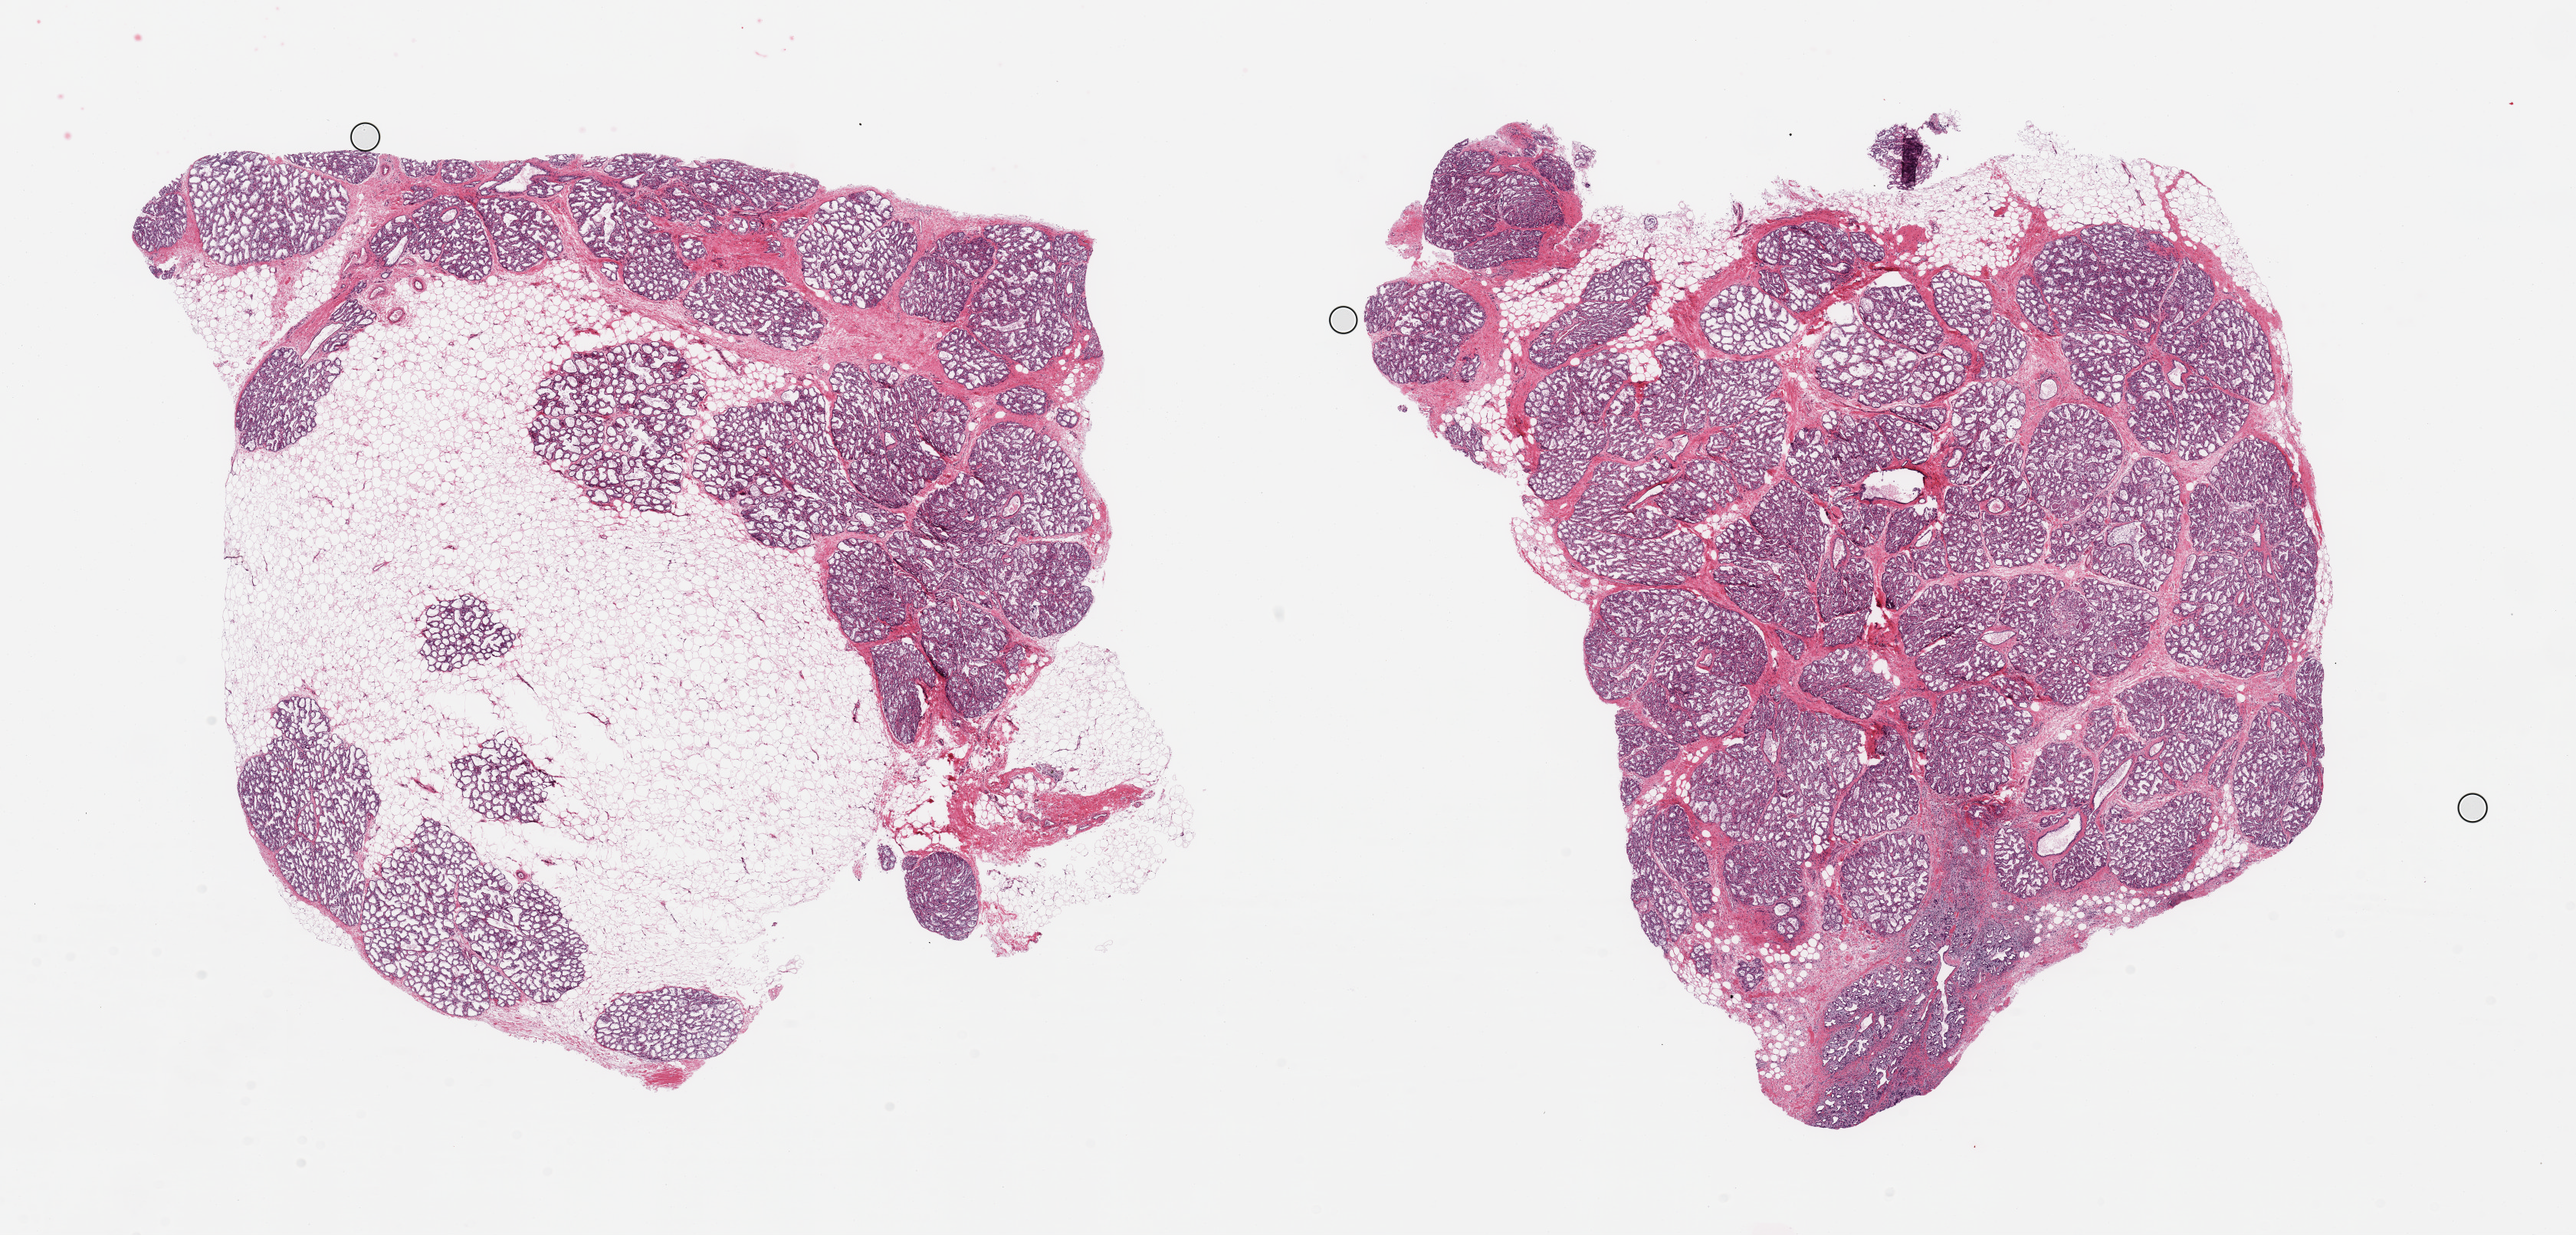
Whole-slide image, H&E stain, brightfield — whole scanned area (about 26.6 x 12.7 mm, slide scanned at 20x) shown as a low-resolution overview; PAXgene-fixed, paraffin-embedded tissue; section of breast (target tissue); tissue donor sample. Donor: female.
Pathologist's review note for this sample: 2 pieces; 50% and 5% adipose tissue; closely packed acini consistent with lactating breast.